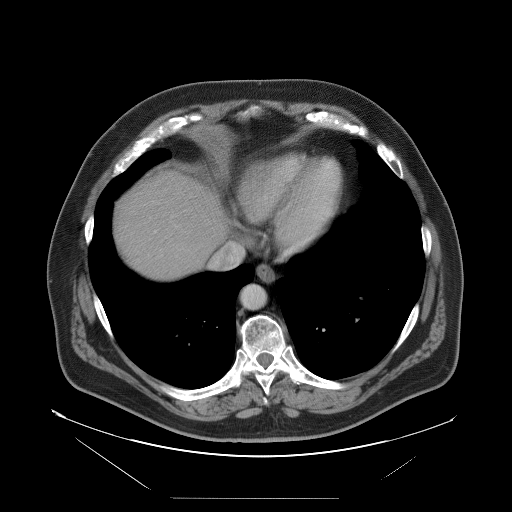
Contrast-enhanced abdominal CT, one axial slice. Slice 92 of 114 in the series (ordered by position). Soft-tissue window (W 400 / L 40 HU). 5 mm slice thickness. 512 × 512 image matrix. Male patient, age 61 years. Case-level facts recorded for this patient, not image findings: diagnosis: colorectal cancer liver metastases, imaged before liver resection; multiple liver metastases: no; largest metastasis: 6.5 cm; disease in both lobes: yes.
Outlined on this slice (manually delineated by an expert):
- hepatic veins: box from (x=211, y=243) to (x=244, y=268) px
- liver: (x=113, y=172)–(x=229, y=278)
- planned liver remnant (the part of the liver to remain after resection): (x=162, y=172)–(x=230, y=248)